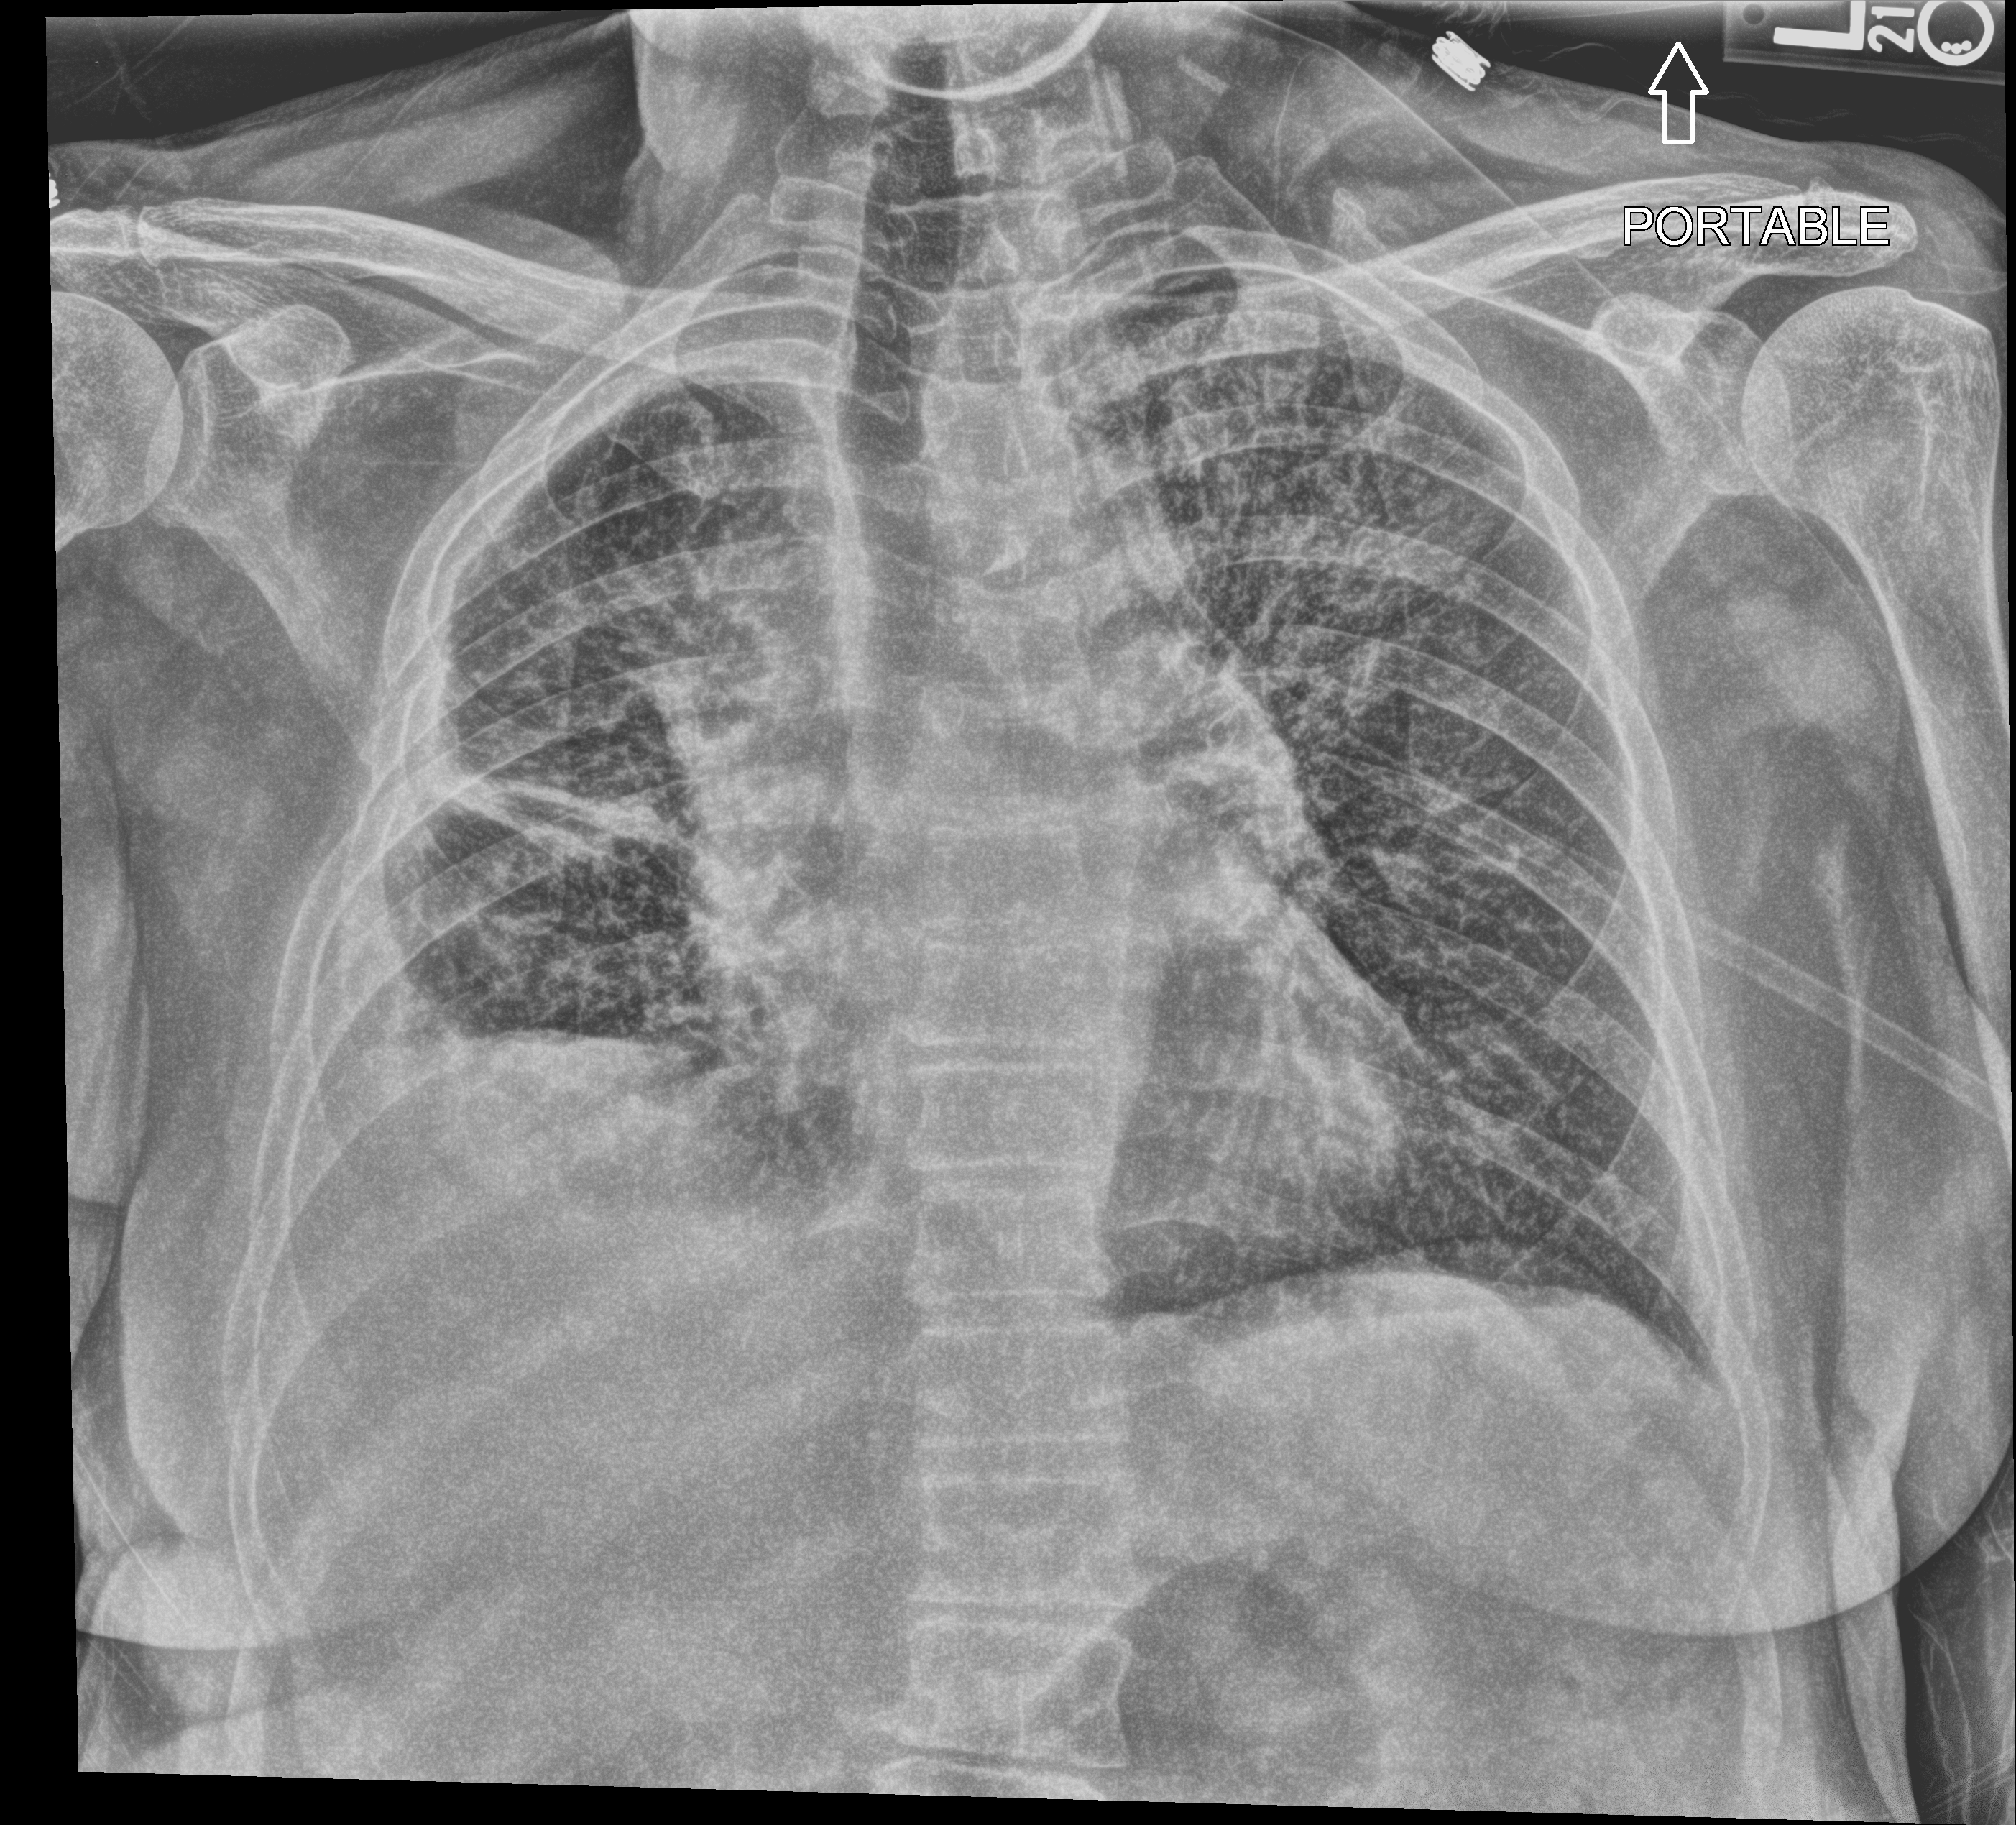
Chest X-ray (portable); anteroposterior (AP) projection. Female patient hospitalised with COVID-19, age 60–74 years.
Admission-level facts for this patient (not findings on this image; timing relative to this image not recorded): mechanically ventilated during this hospital stay: no; admitted to intensive care during this hospital stay: no.